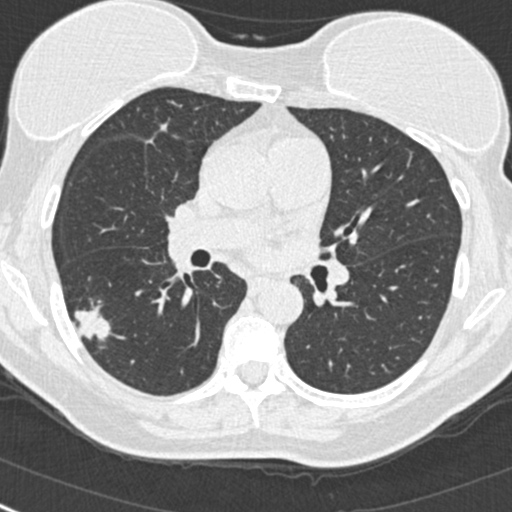
Low-dose screening chest CT, one axial slice; slice 146 of 268 in the series (ordered by position); lung window (W 1500 / L -600 HU); 1 mm slice thickness; 512 × 512 image matrix.
Structures marked on this image (outlined manually by an expert reader):
- lesion 1 (tumor, upper lobe of right lung): bounding box [x1, y1, x2, y2] px = [75, 305, 111, 340]